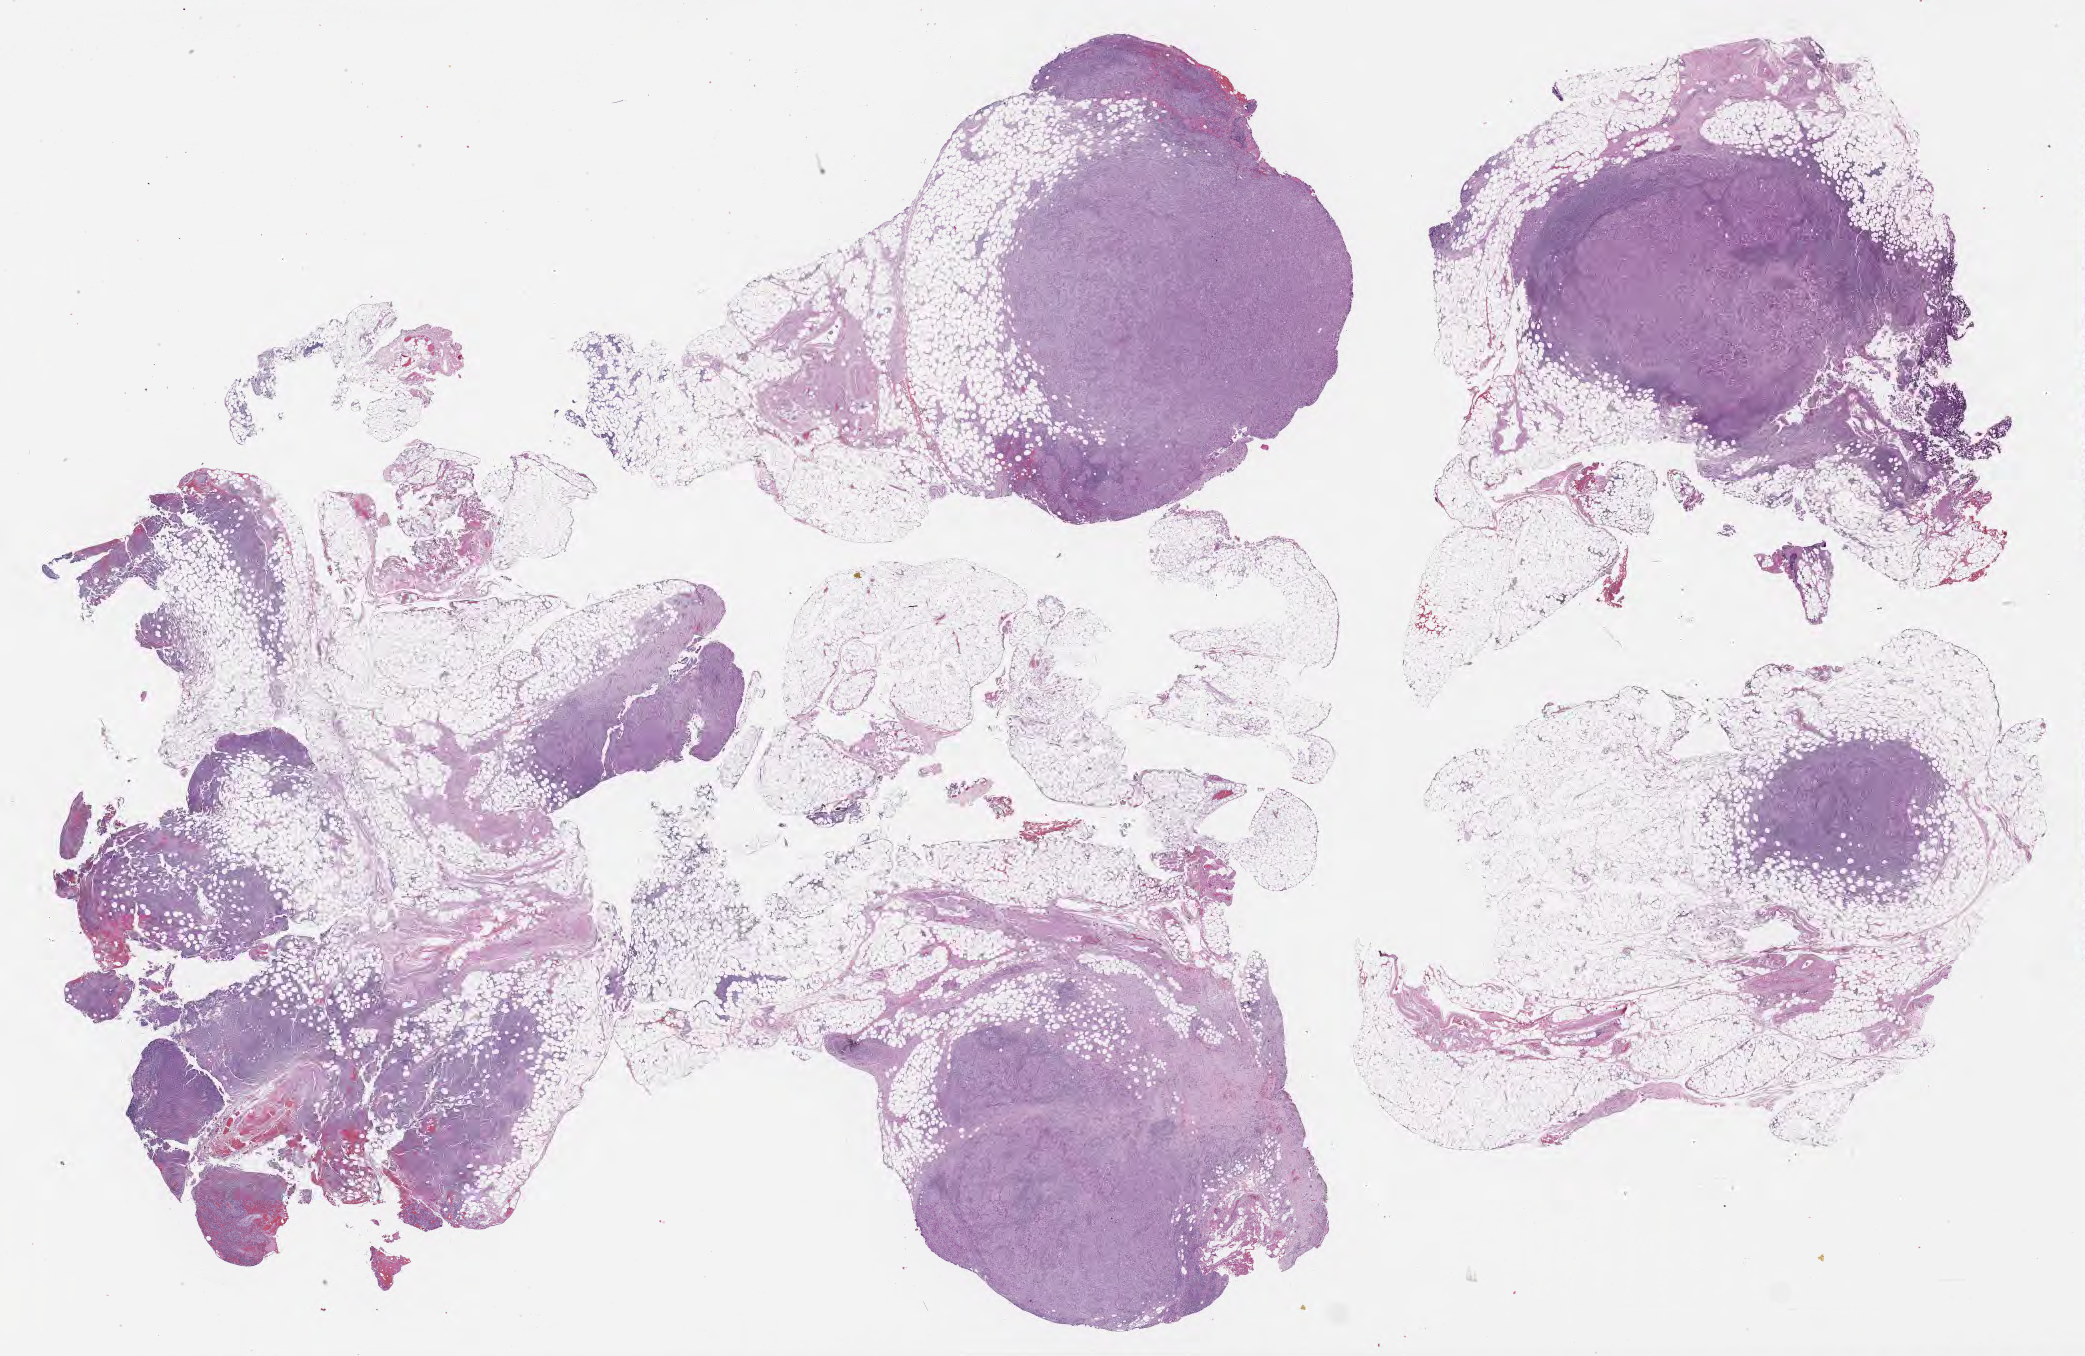
Whole-slide image, haematoxylin and eosin stain, shown as a low-resolution overview of the whole scanned area (about 33.7 x 21.9 mm), specimen: tumor tissue, site: lung (left). Male patient, aged 58.
Histologic diagnosis: Adenocarcinoma, NOS.